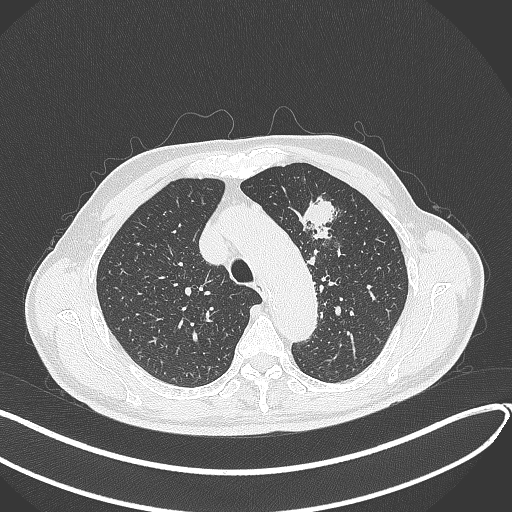
Chest CT, one axial slice; position 314 of 459 along the scan axis; reconstruction kernel B70f; lung window (W 1500 / L -600 HU); 512 × 512 image matrix, field of view 400 × 400 mm. Patient: male, 74 years. From the clinical record (not read from this slice): clinical TNM (as recorded): T2b N0 M1c.
Structures marked on this image (rectangle marked by the reading radiologist):
- lung tumour (recorded histology: adenocarcinoma): bounding box <295,192,340,250> (left, top, right, bottom; pixels)